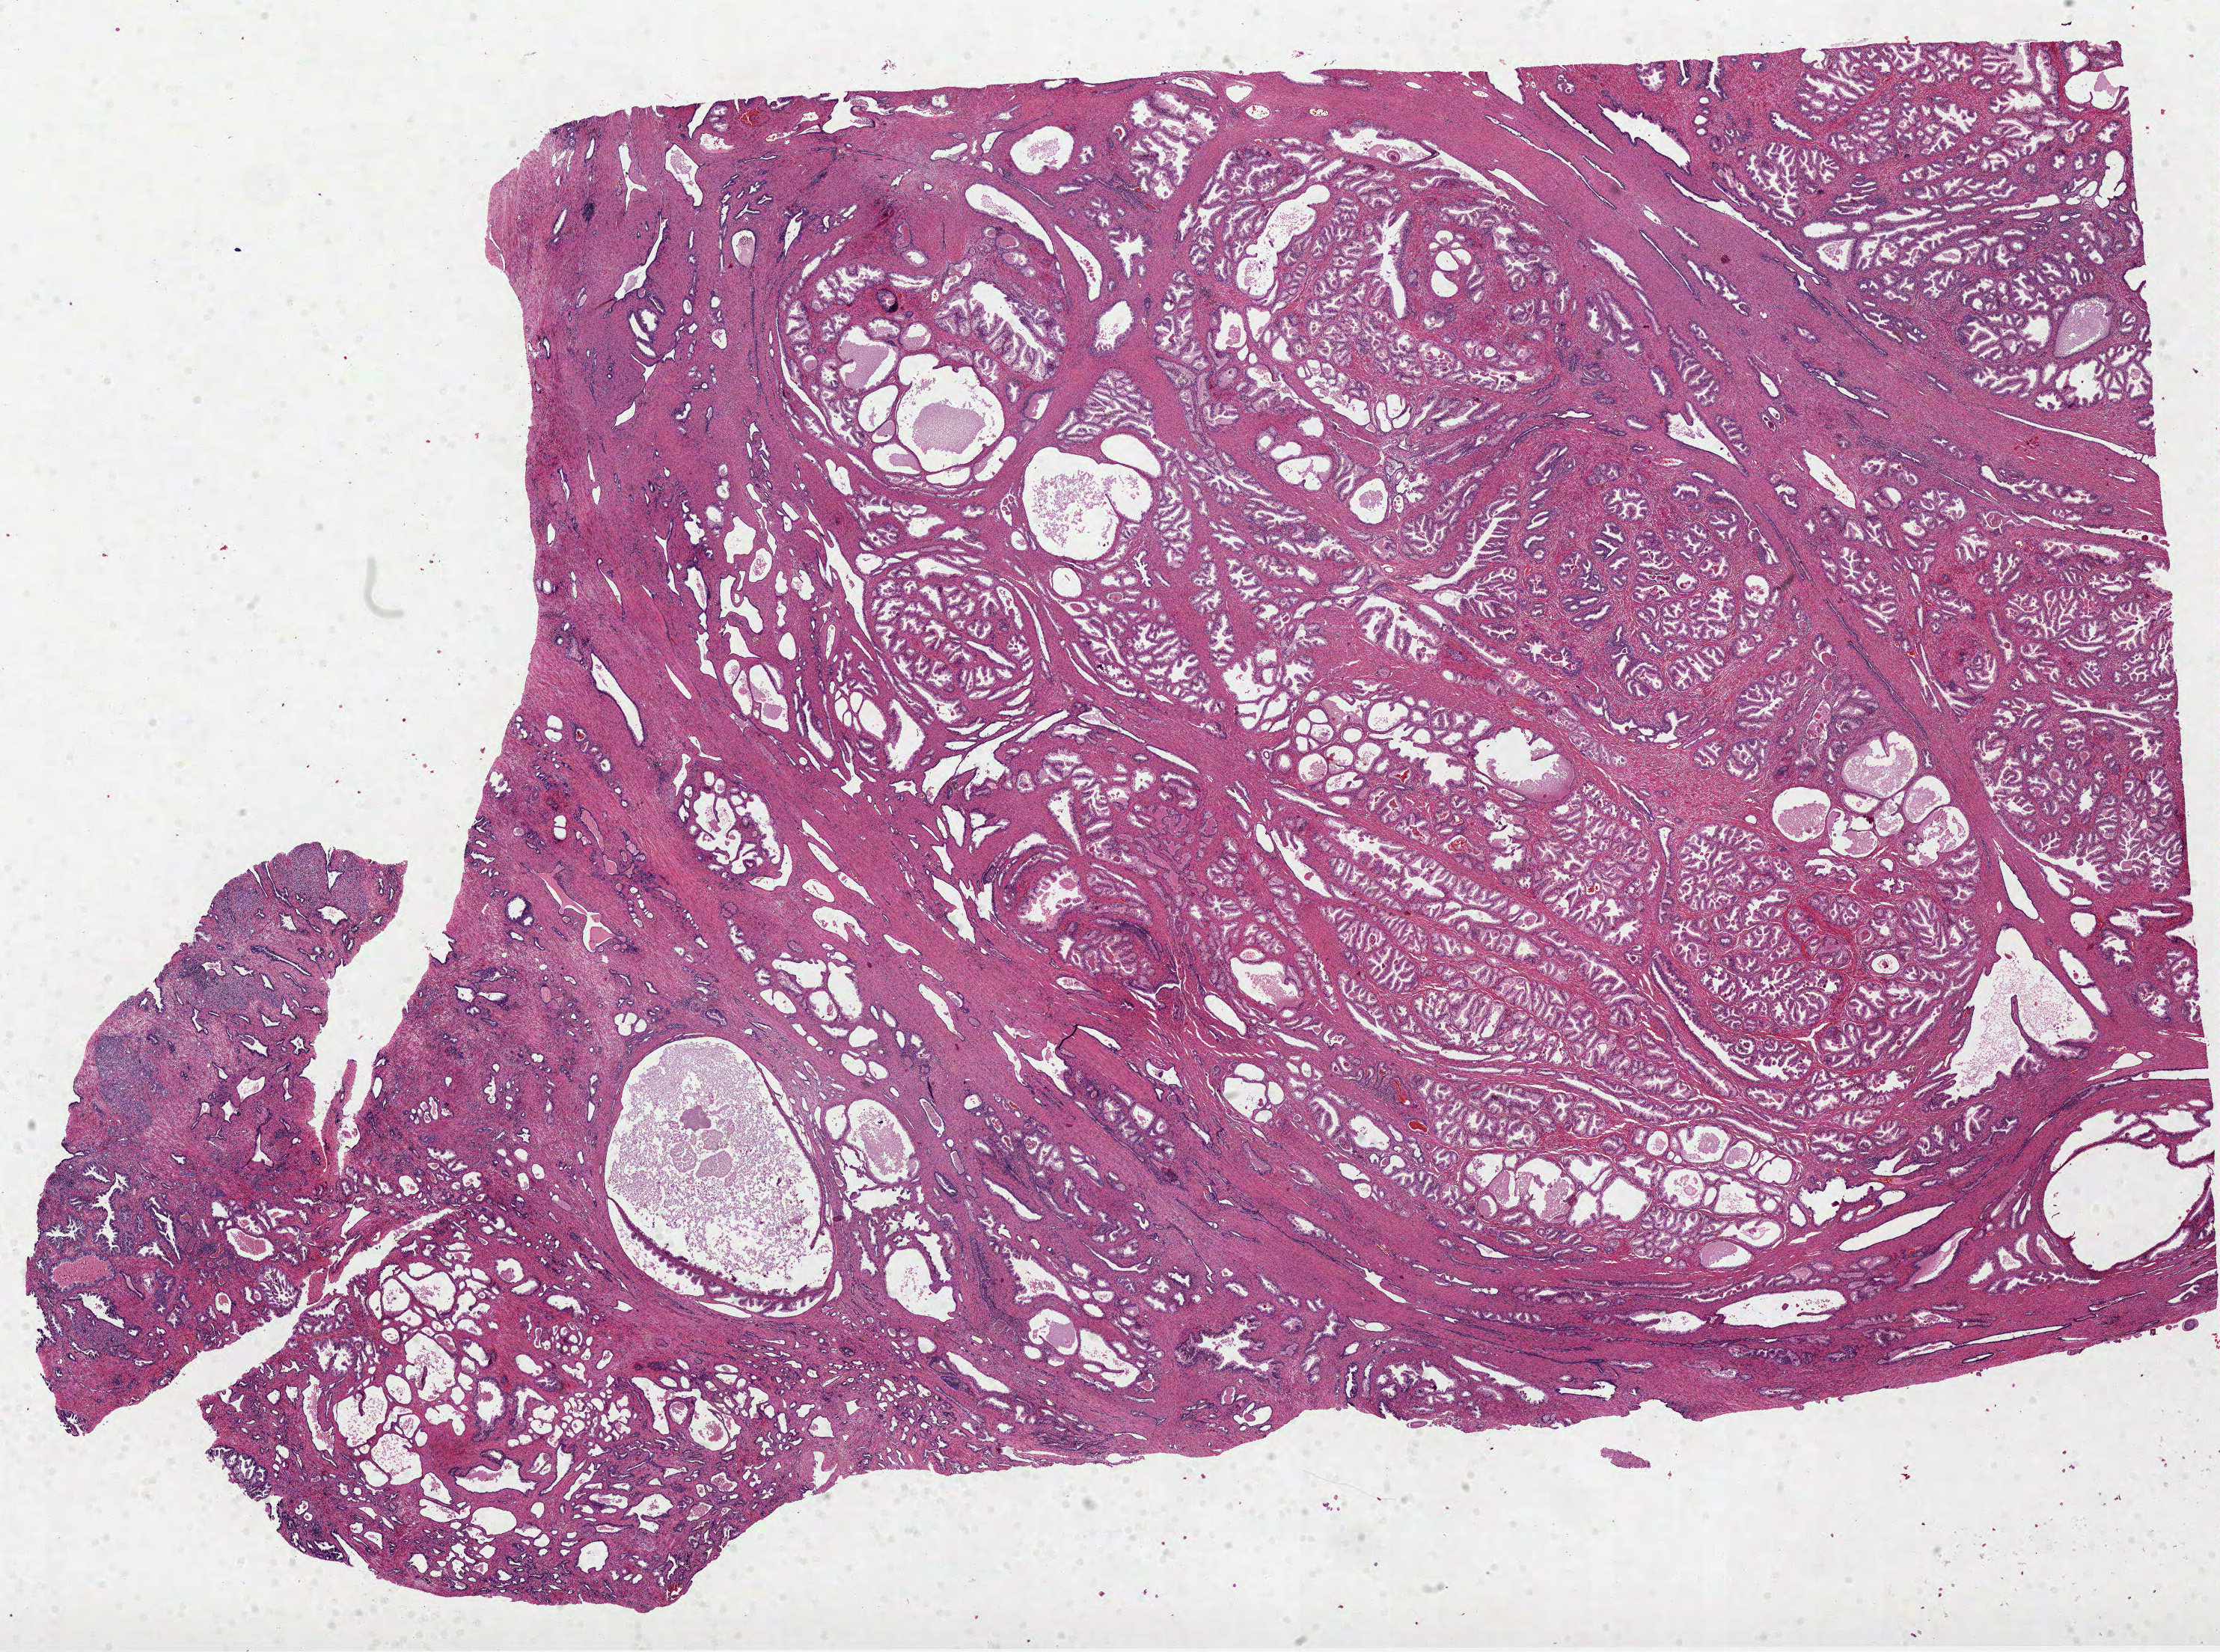
Digitized Hematoxylin and eosin (H&E) stained tissue section (whole slide) — a low-resolution overview of the entire scanned area, about 23.9 x 17.8 mm (from a 40x scan). FFPE section. Primary tumour sample from the prostate. Patient: male, age at initial diagnosis 56 years. Gleason score: 8 (4+4).
Laterality: bilateral. Diagnosis: Acinar cell carcinoma. Lymph nodes positive (case pathology): 1 of 27 examined.